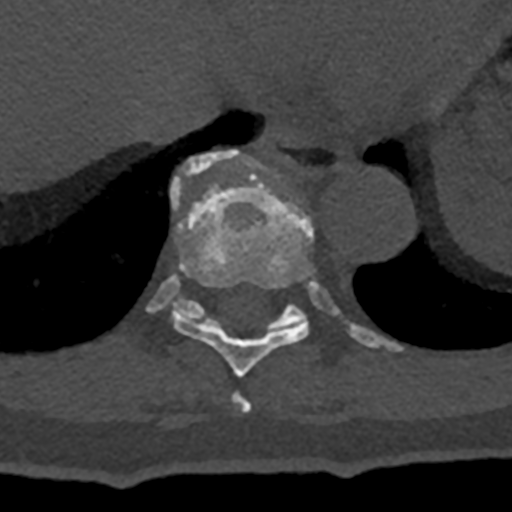
CT including the spine, one axial slice; slice 639 of 797 in the series (ordered by position); reconstruction kernel Br40s/3; 120 kVp; bone window (W 1800 / L 400 HU); 0.5 mm slice thickness; 512 × 512 image matrix, field of view 160 × 160 mm. Male patient, age 74 years. From the clinical record (not read from this slice): primary cancer: renal.
Structures marked on this image (semi-automatic segmentation, software-assisted and operator-edited):
- T10 vertebra: bounding box [x1, y1, x2, y2] px = [146, 150, 403, 352]
- T8 vertebra: [232, 392, 252, 413]
- T9 vertebra: [171, 186, 314, 377]